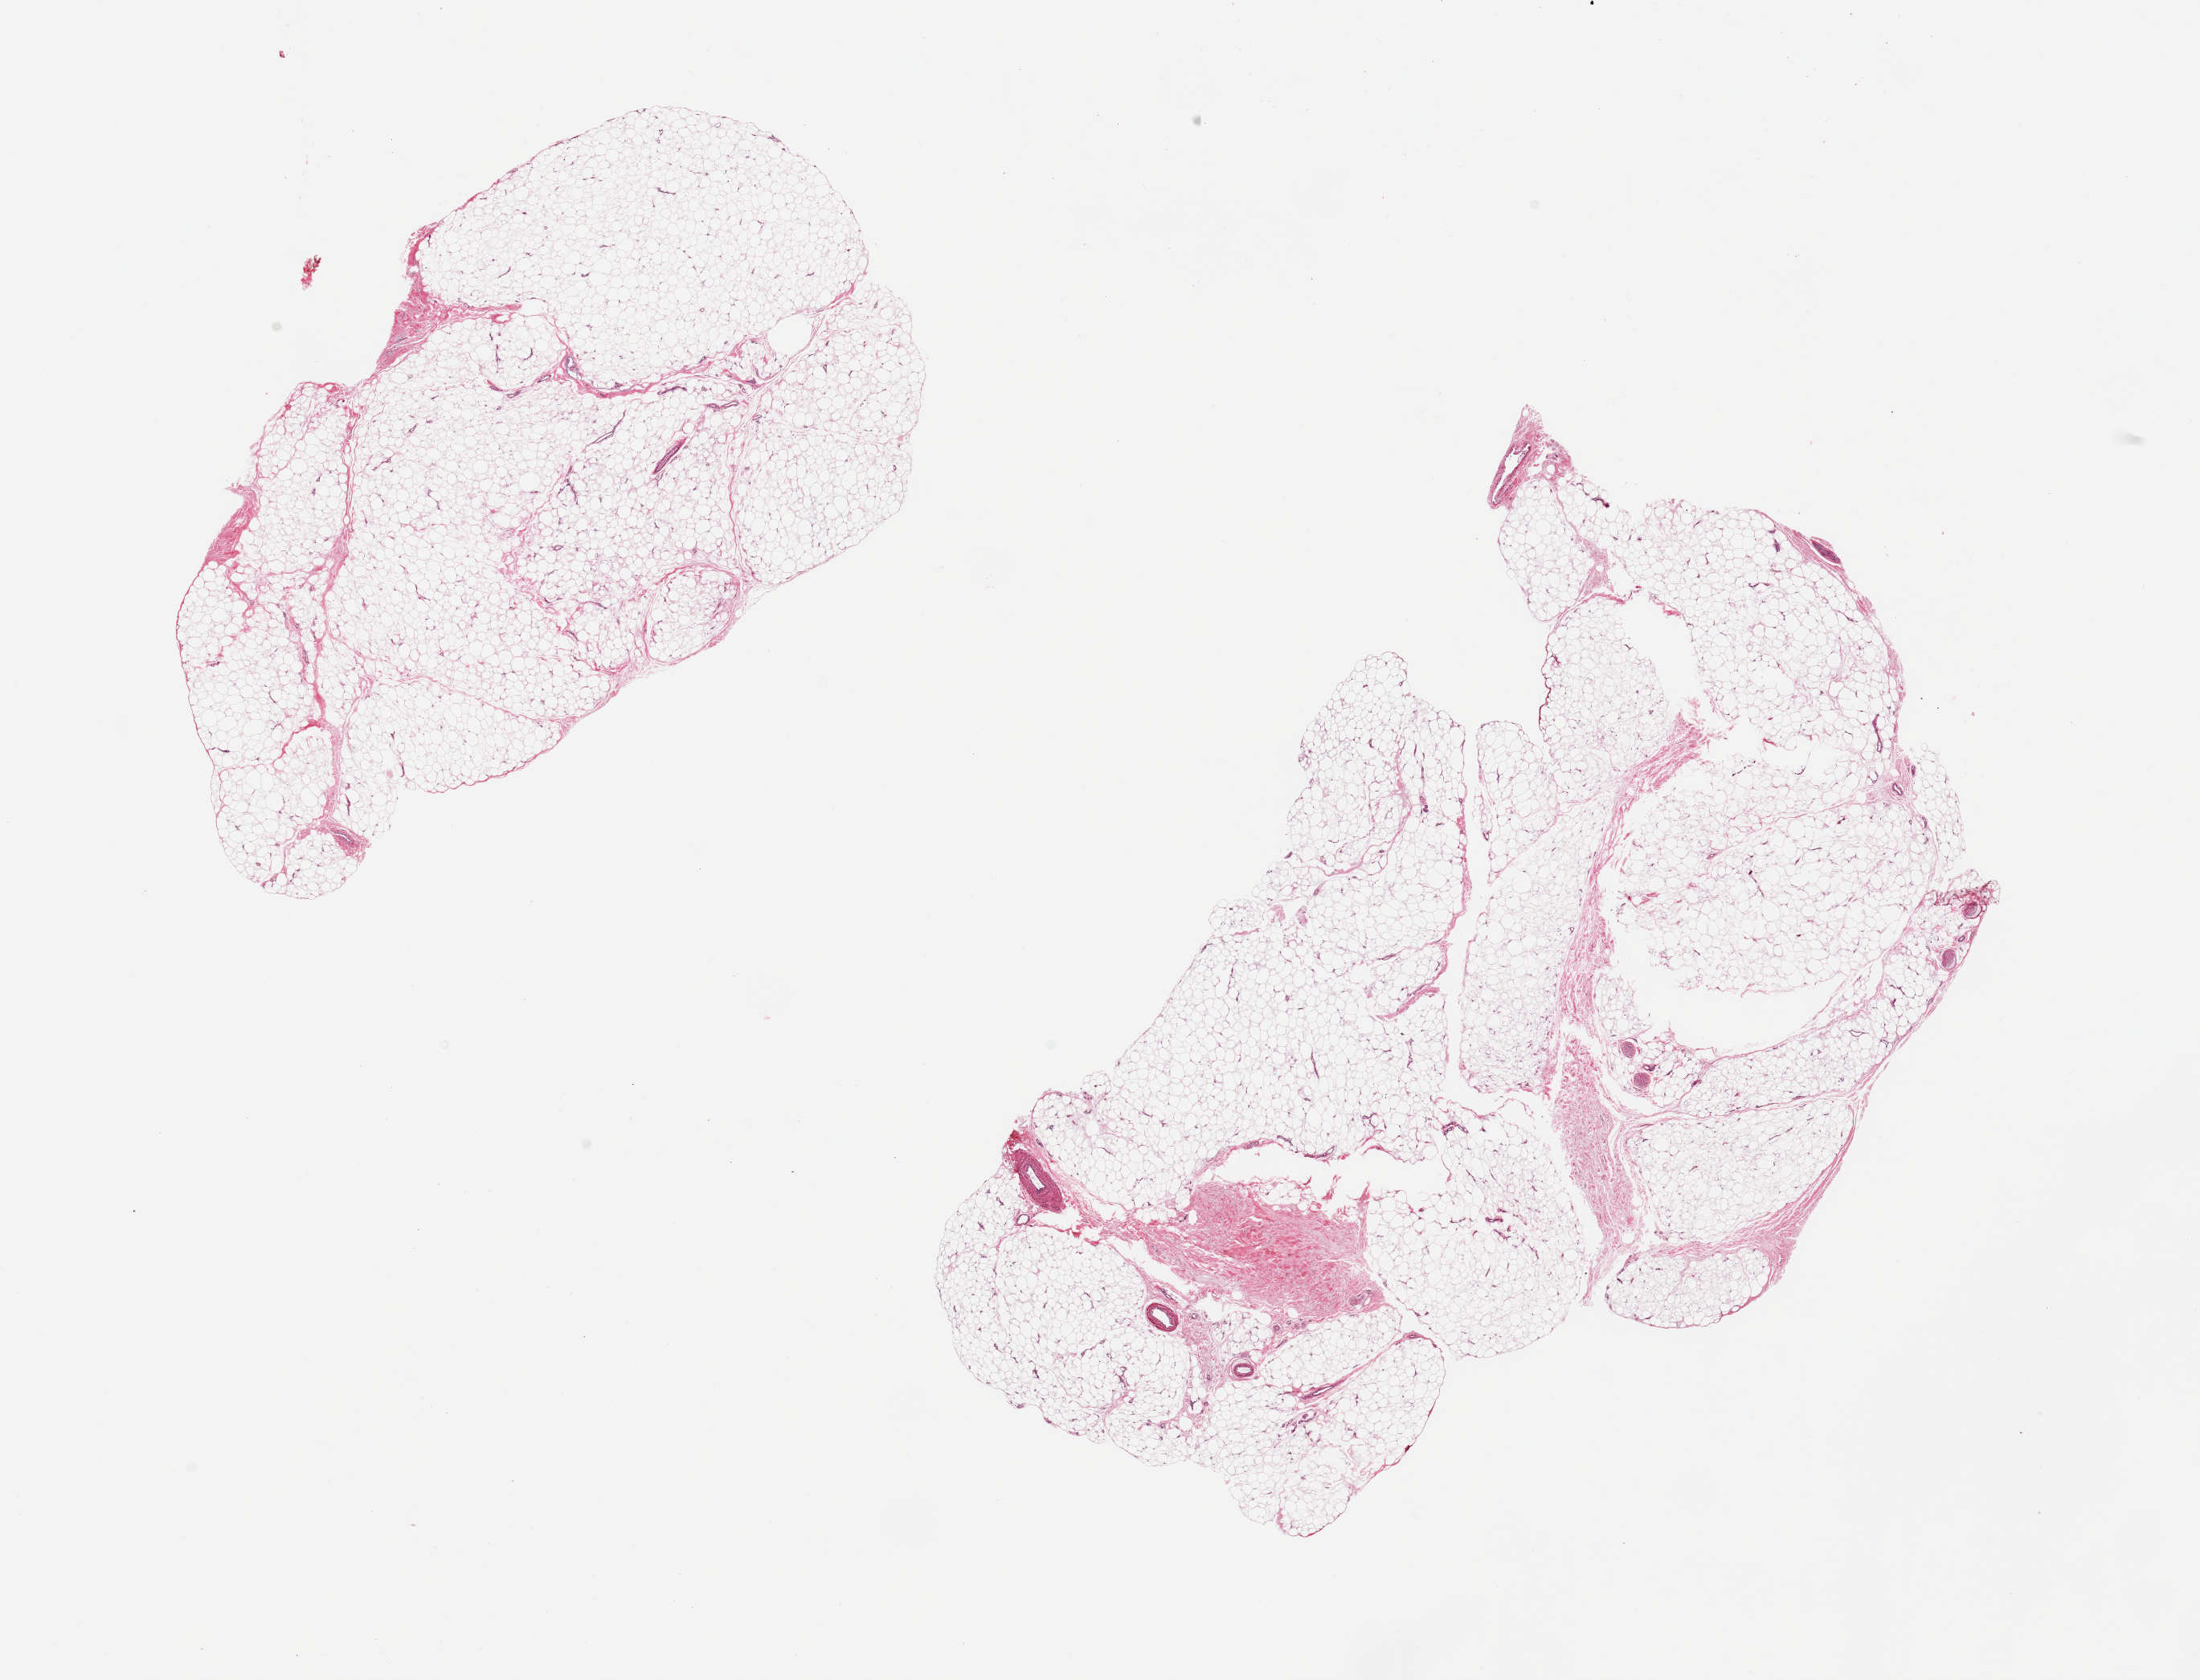
Whole-slide image, hematoxylin and eosin (H&E) stain, brightfield, a low-resolution overview of the entire scanned area, about 21.7 x 16.5 mm (from a 20x scan), PAXgene-fixed, paraffin-embedded tissue, section of adipose tissue (target tissue), donor tissue sample.
* reviewer comment on this tissue sample: 2 pieces; includes few small vessels and nerve